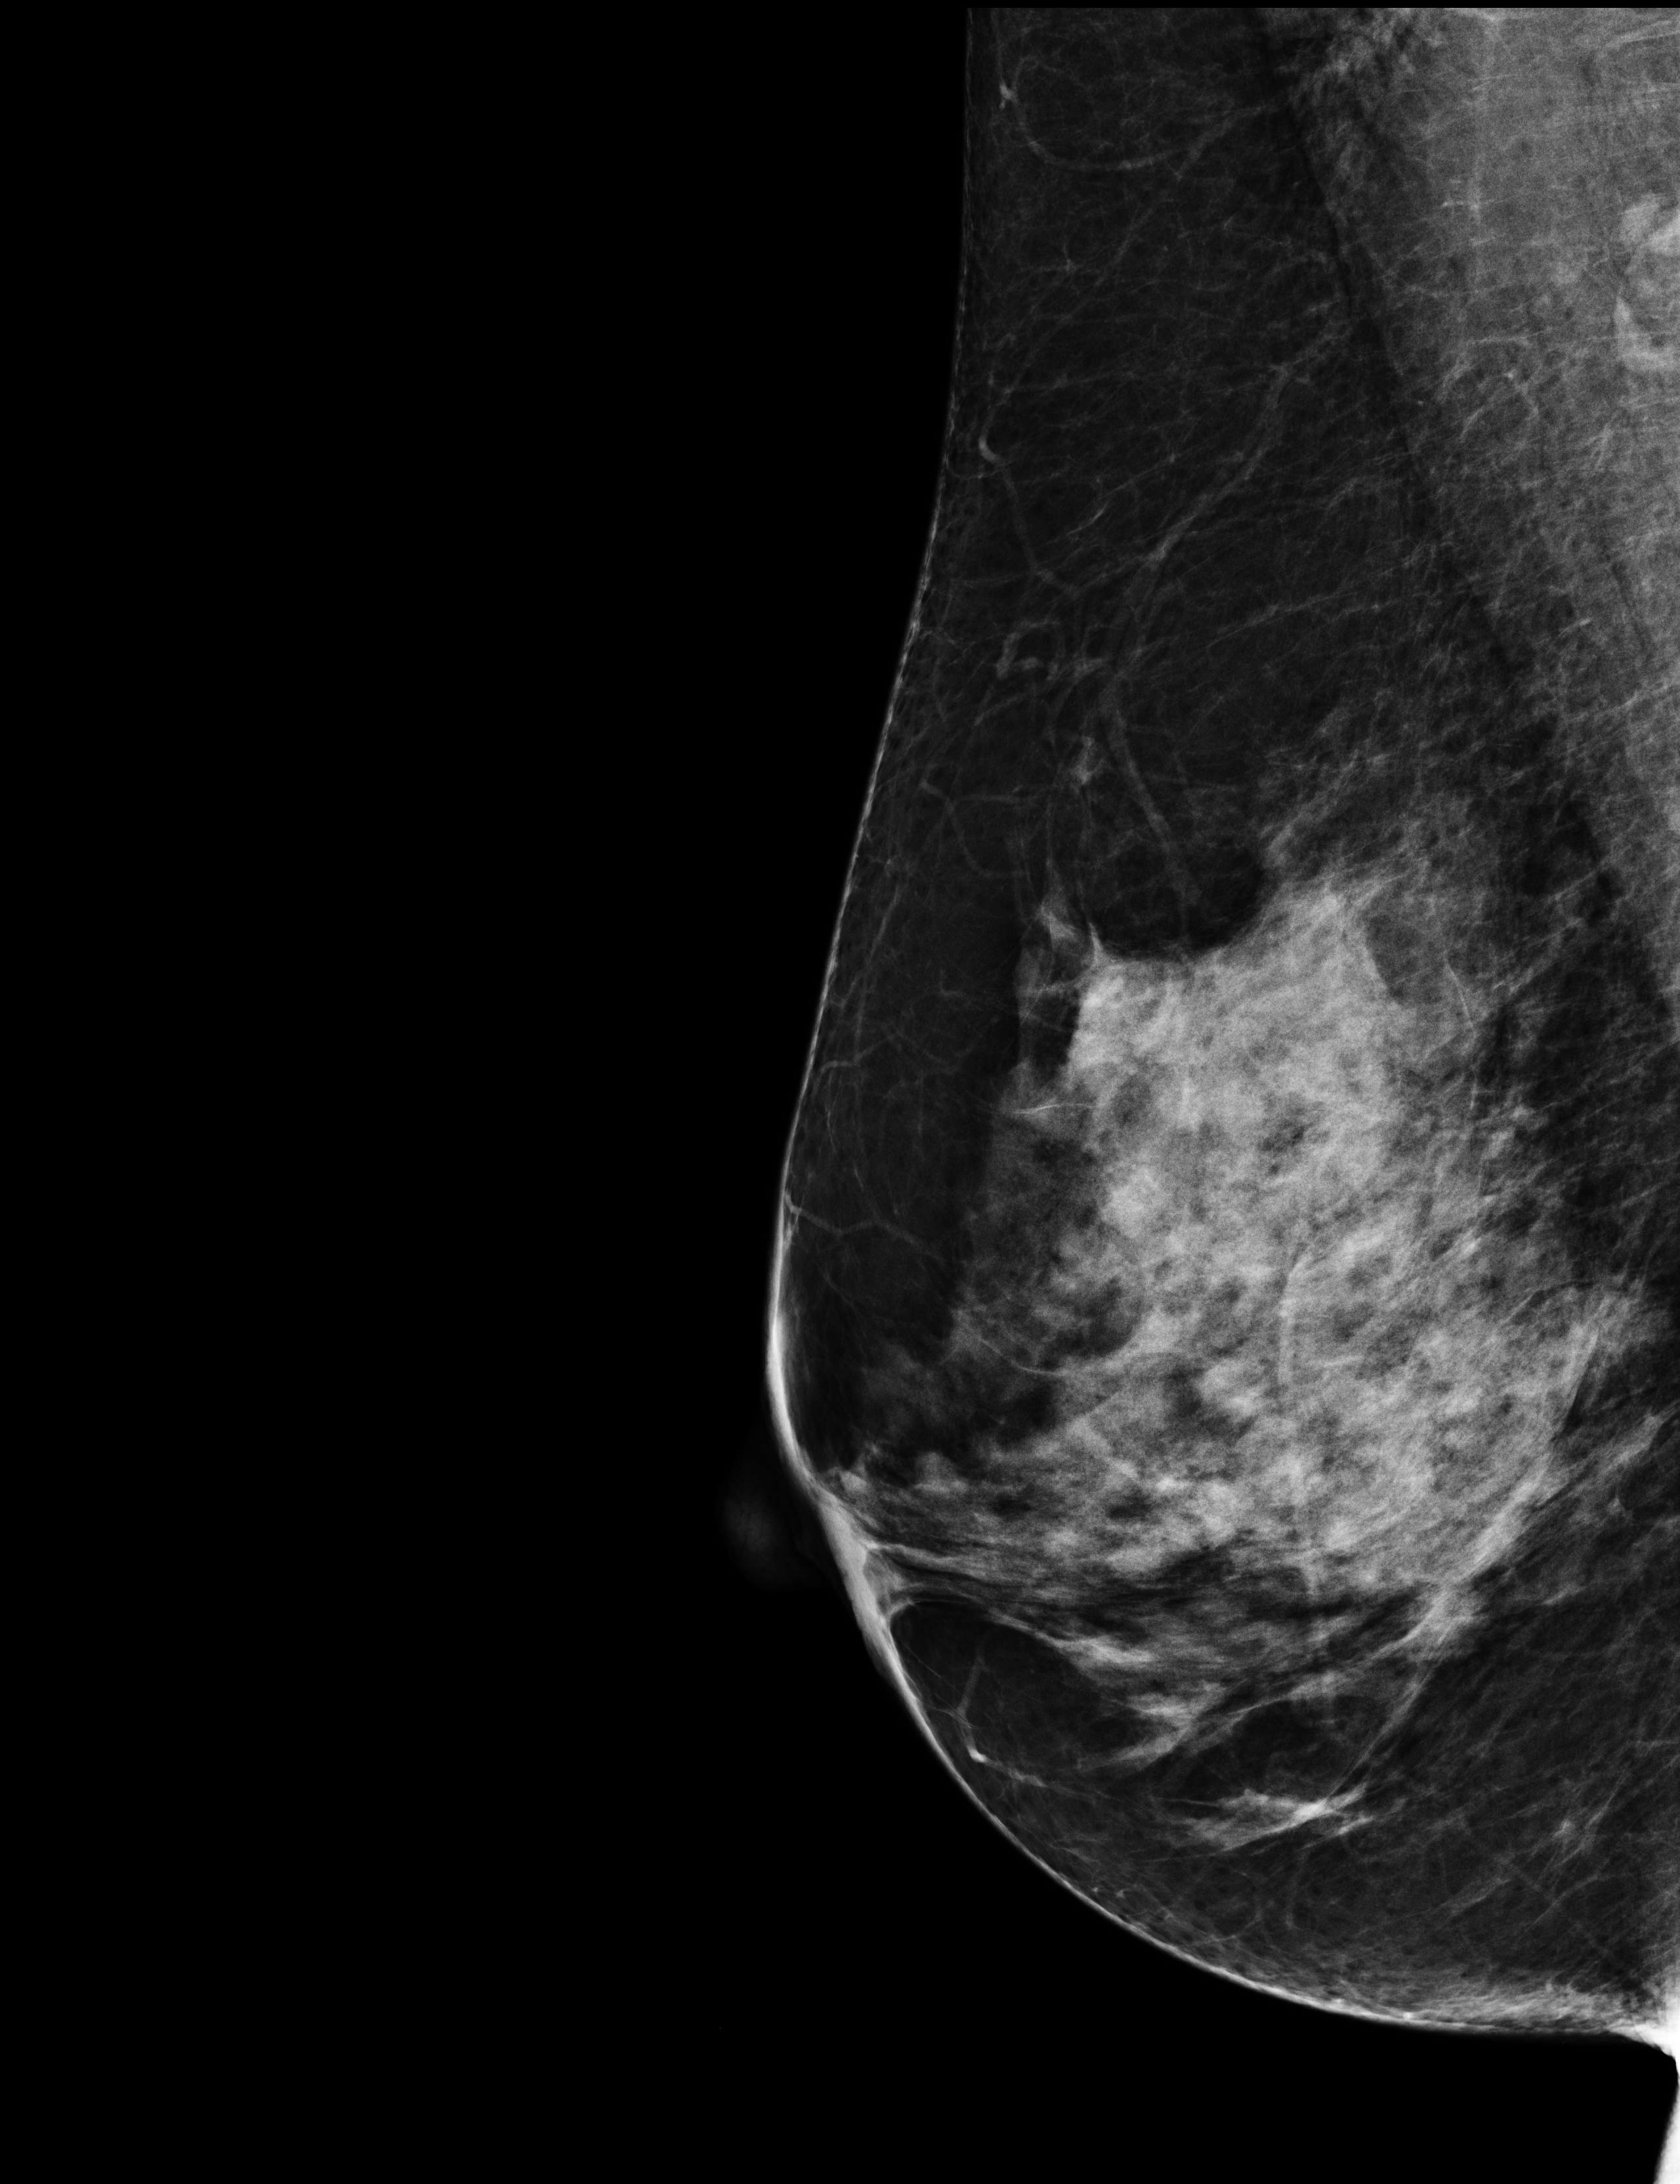
Screening examination. Patient aged 51 years (female).
Image type: full-field digital mammogram. Breast: right. Projection: medio-lateral oblique projection.